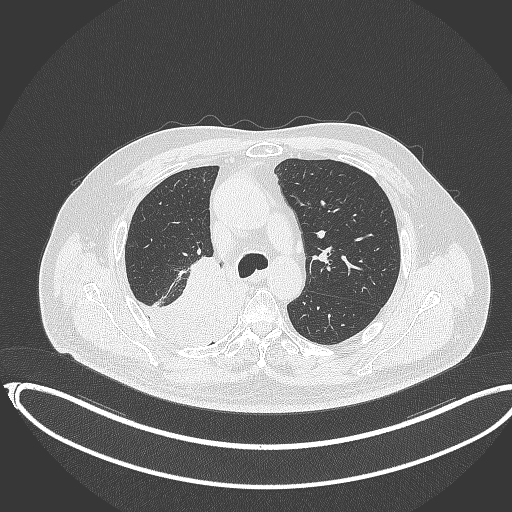
Chest CT, one axial slice; slice 244 of 403 in the series (ordered by position); lung window (W 1500 / L -600 HU); 512 × 512 image matrix, field of view 436 × 436 mm. Male patient, age 68 years. Case-level facts recorded for this patient, not image findings: clinical TNM (as recorded): T2a N0 M0.
Structures marked on this image (rectangle marked by the reading radiologist):
- lung tumour (recorded histology: adenocarcinoma): bounding box (x1, y1, x2, y2) in pixels: (131, 257, 236, 350)